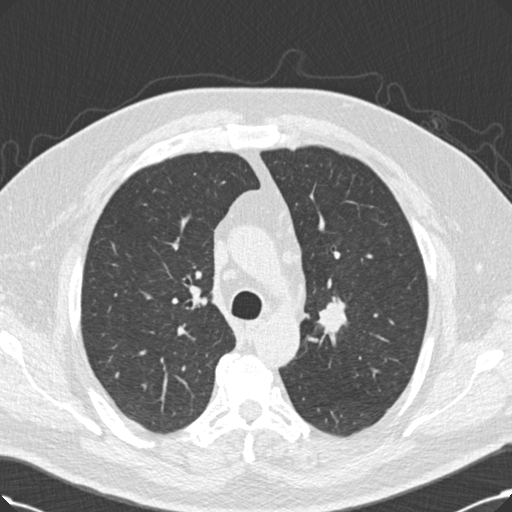
Low-dose screening chest CT, one axial slice; slice 156 of 214 in the series (ordered by position); 120 kVp; lung window (W 1500 / L -600 HU); 2 mm slice thickness; 512 × 512 image matrix.
Structures marked on this image (outlined manually by an expert reader):
- lesion 1 (tumor): bounding box [x1, y1, x2, y2] px = [318, 297, 347, 341]